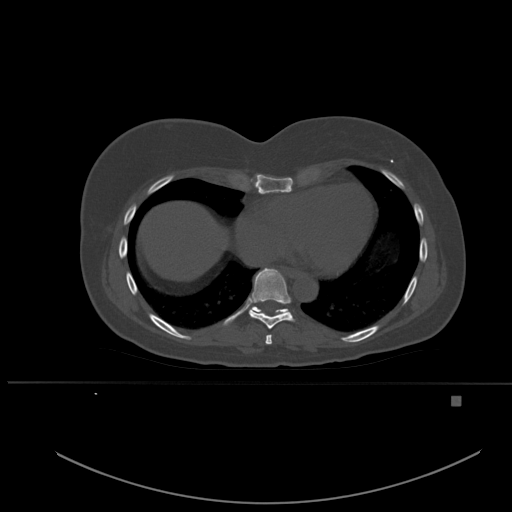
CT including the spine, one axial slice. Position 318 of 651 along the scan axis. Bone window (W 1800 / L 400 HU). 1.5 mm slice thickness. 512 × 512 image matrix. Female patient, age 49 years. Case-level facts recorded for this patient, not image findings: primary cancer: breast; vertebrae with lytic lesions (as recorded): L3, T12, L4.
Outlined on this slice (semi-automatic segmentation, software-assisted and operator-edited):
- T7 vertebra: bounding box (x1, y1, x2, y2) in pixels: (265, 334, 272, 344)
- T8 vertebra: (248, 268, 295, 329)
- T9 vertebra: (249, 306, 289, 313)